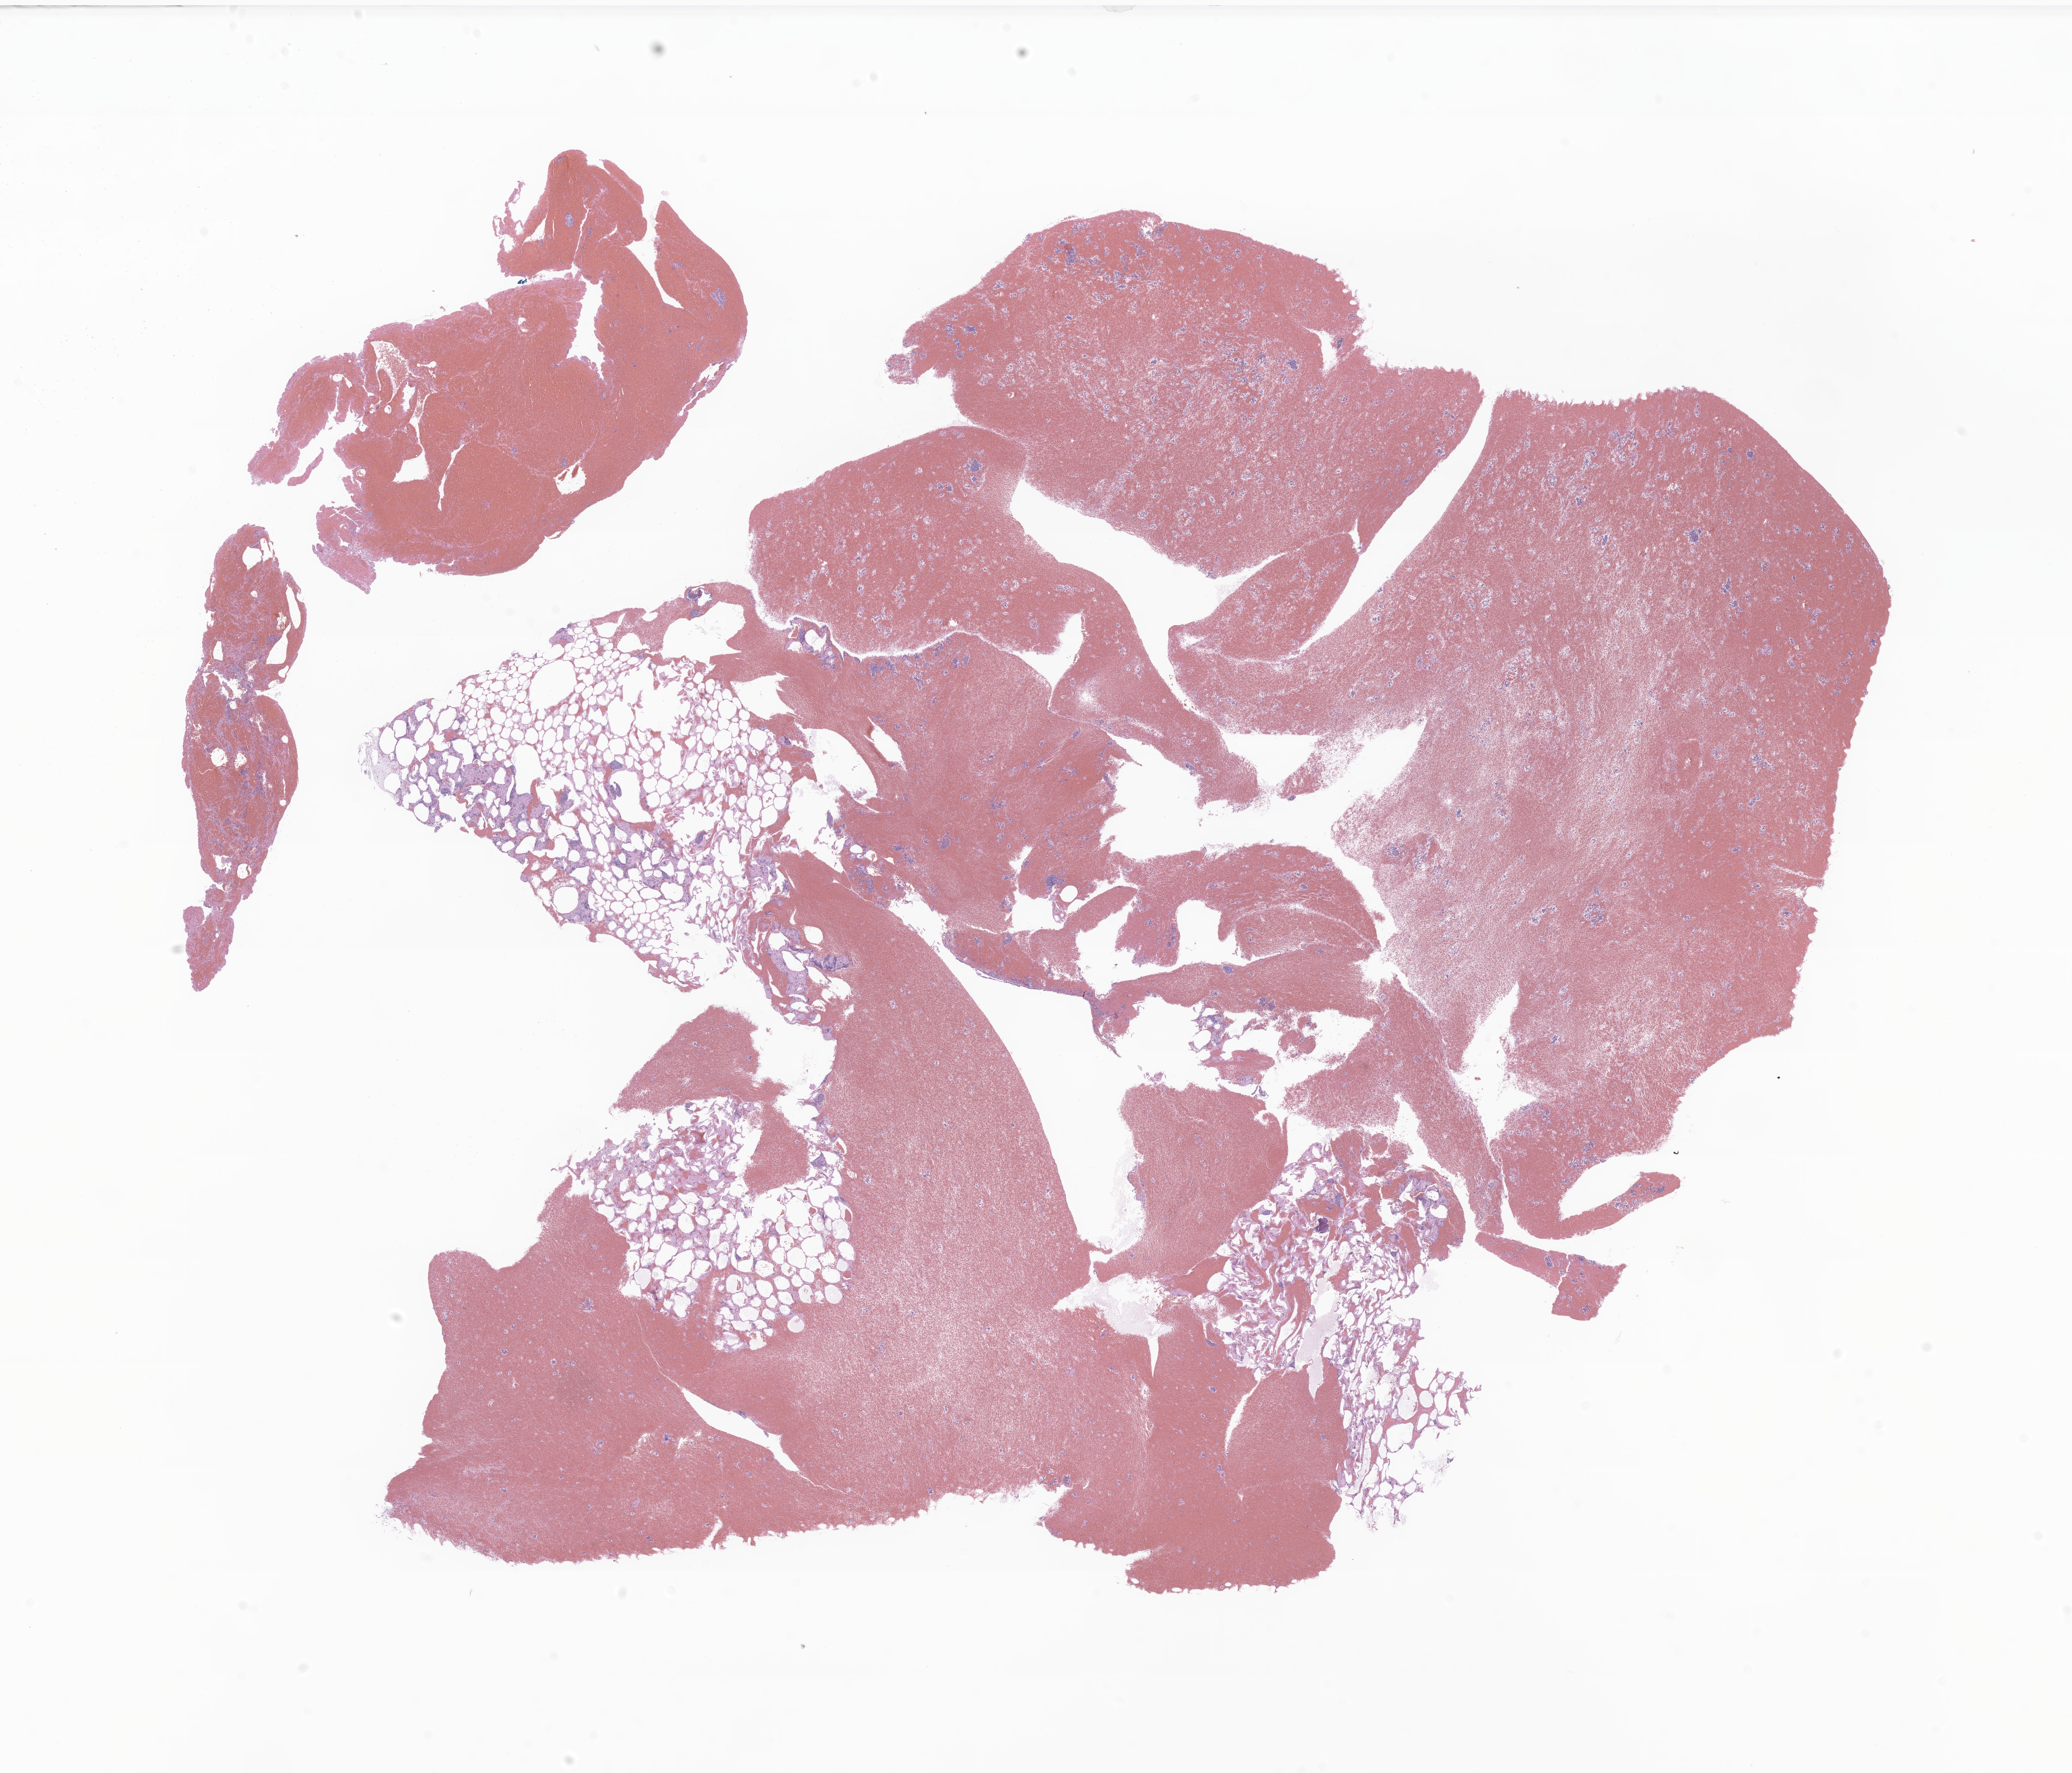
Digitized H&E-stained section of tumor tissue from the adrenal gland — a low-resolution overview of the entire scanned area, about 21.3 x 18.2 mm, formalin-fixed paraffin-embedded section. Patient: male, age 378 days (about 1.0 years).
Diagnosis (ICD-O-3 morphology term): Neuroblastoma, NOS.